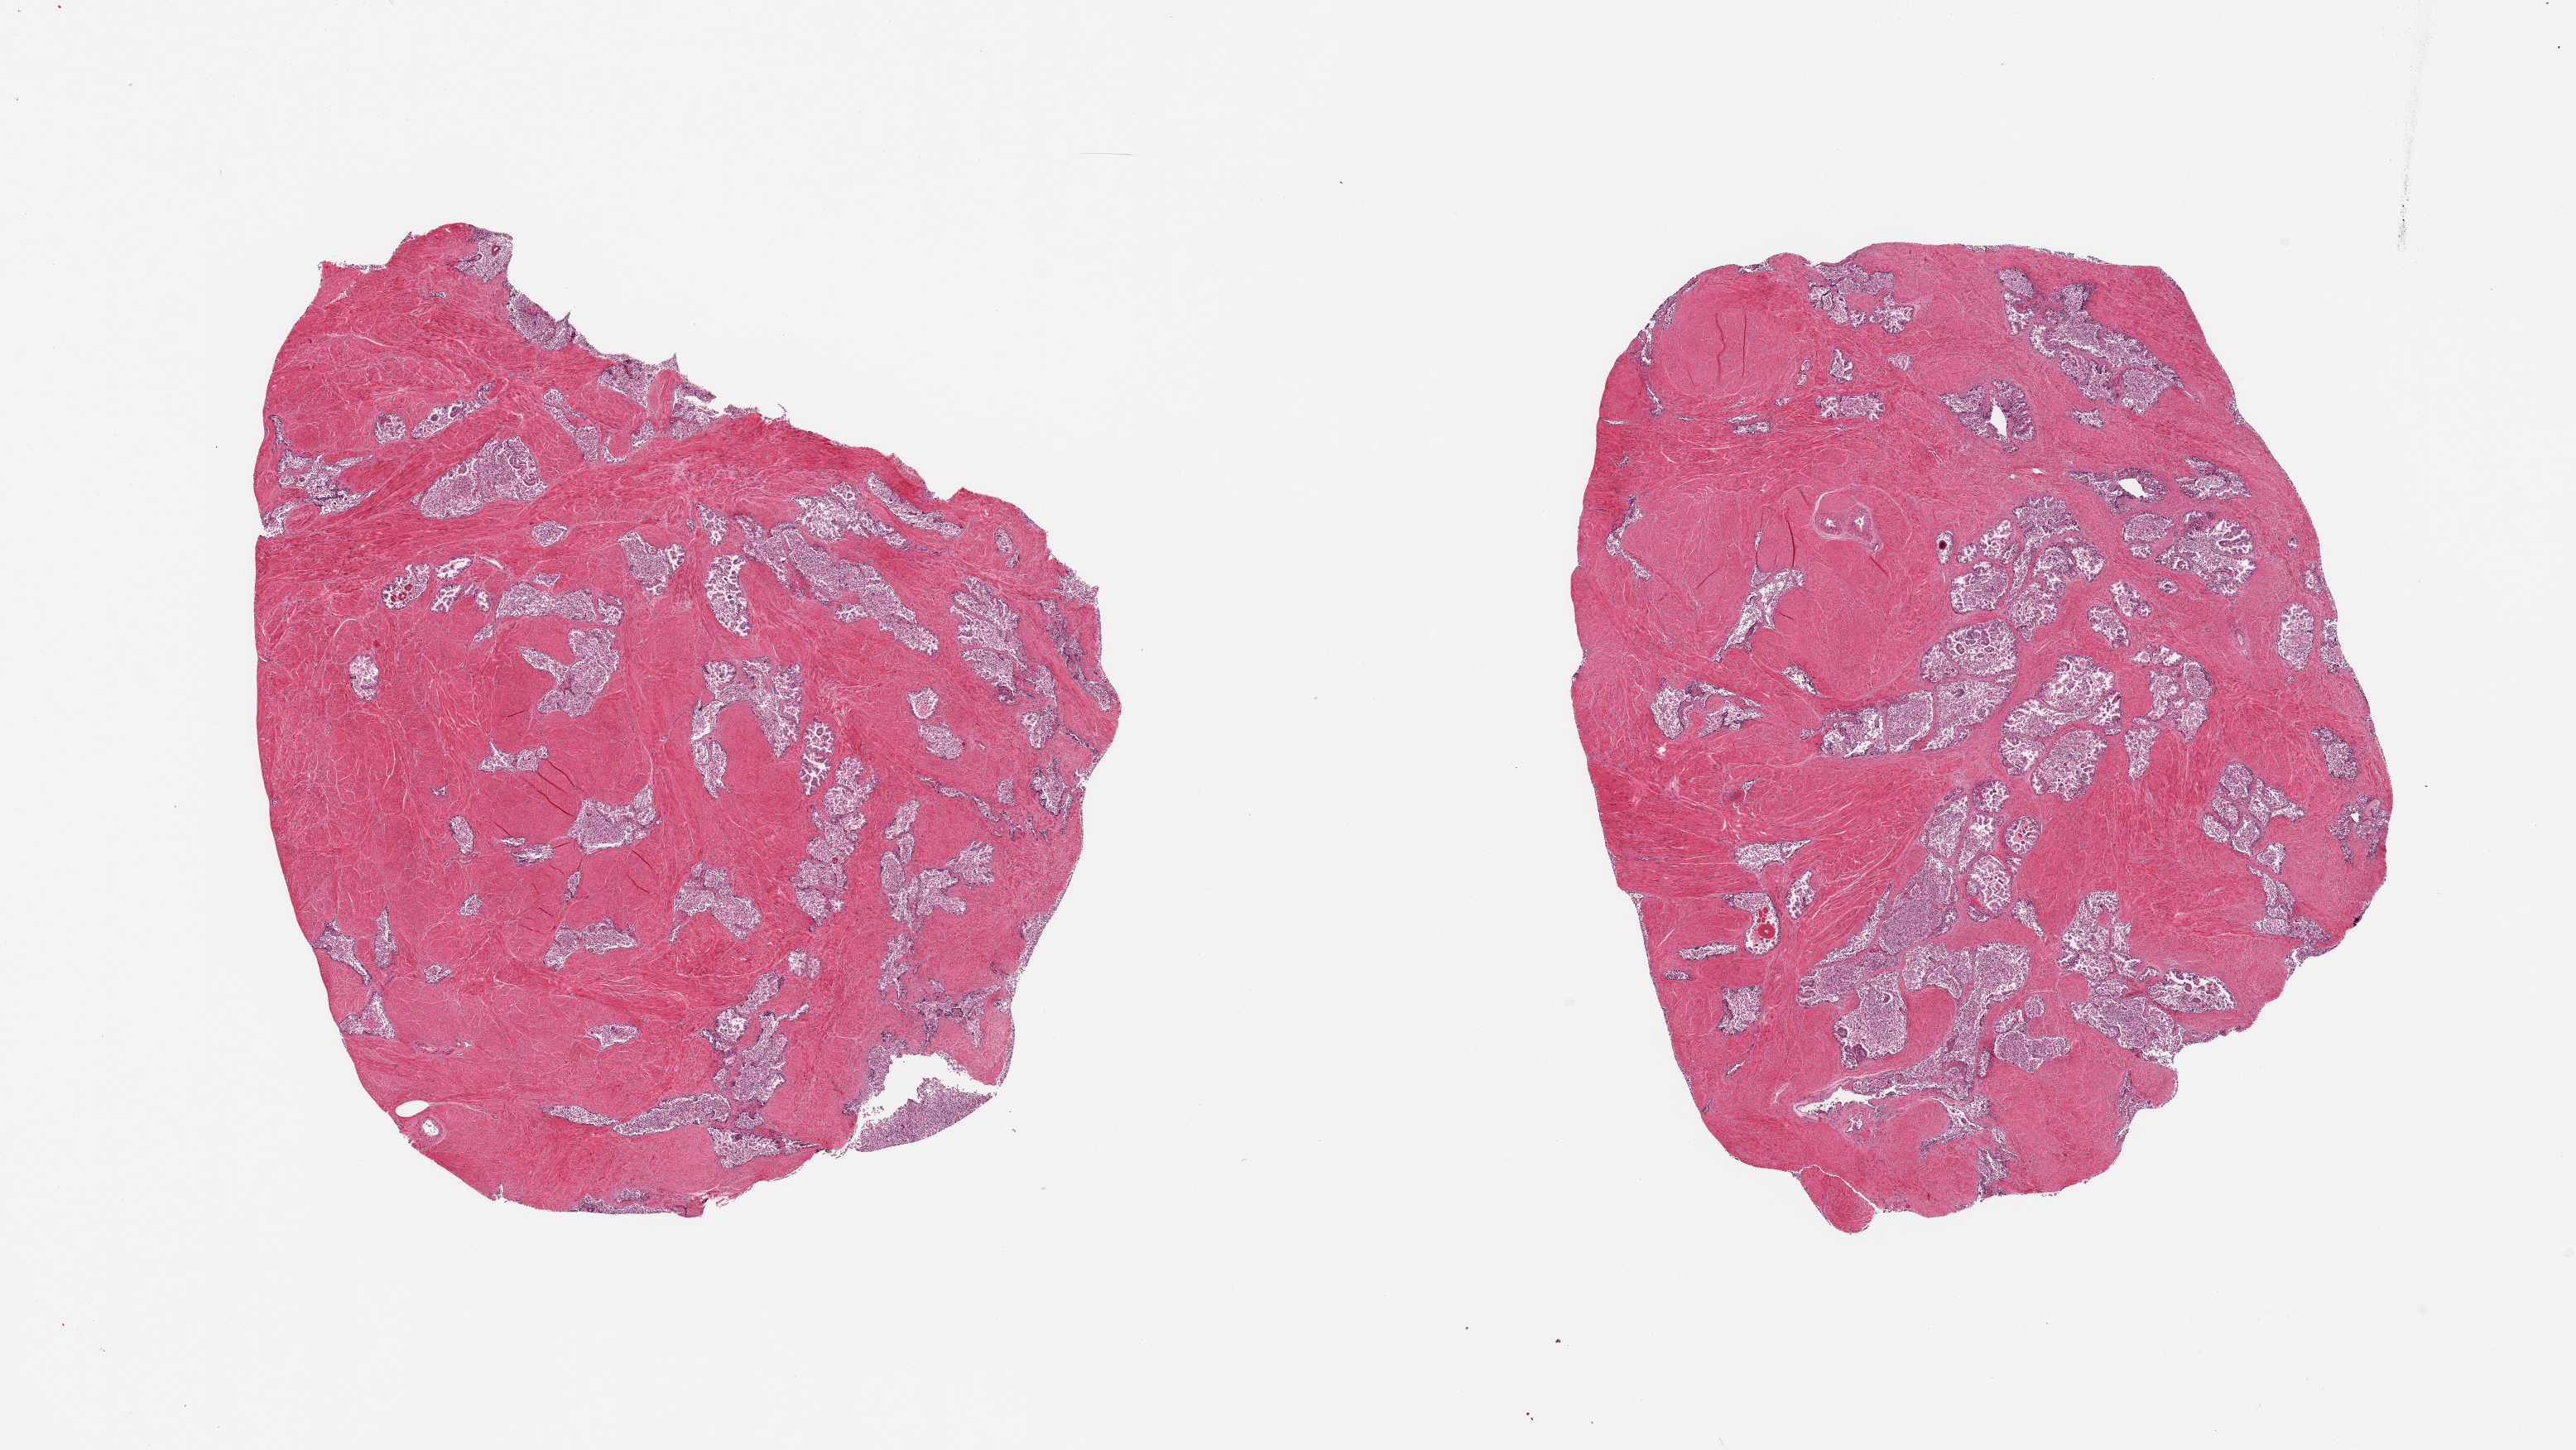
Hematoxylin and eosin (H&E) whole-slide image — low-resolution overview of the scanned area, about 24.6 x 13.9 mm, PAXgene-fixed, paraffin-embedded tissue, sampled site (target tissue): prostate, donor tissue sample. Donor sex: male.
Reviewer comment on this tissue sample: 2 pieces; well preserved fibromuscular stroma and glandular component with mostly sloughed autolyzed epithelium.